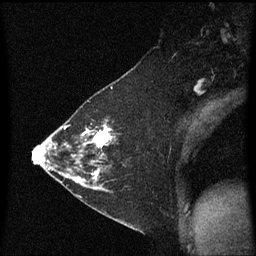
Breast MRI (dynamic contrast-enhanced), one sagittal slice; slice 39 of 60 in the series (ordered by position); dynamic contrast-enhanced series, image 2 of 3 at this slice position (ordered by acquisition); 1.5 T; TE 4.2 ms, TR 8.4 ms; 256 × 256 image matrix, field of view 200 × 200 mm. Female patient, age 36 years. Case-level facts recorded for this patient, not image findings: setting: breast cancer imaged before/during neoadjuvant chemotherapy; receptor status: HR-positive, HER2-negative.
Structures marked on this image (semi-automatically segmented with operator editing):
- analysis volume of interest (the breast-tissue region the enhancement analysis was run in; not a lesion): box from (x=72, y=116) to (x=117, y=187) px
- tumour enhancement mask (voxels above the 70 % enhancement threshold inside the analysis volume of interest): (x=74, y=122)–(x=115, y=183)